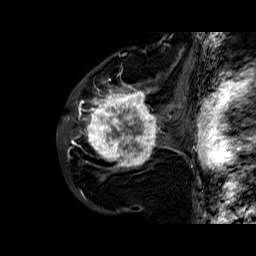
Breast MRI (dynamic contrast-enhanced), one sagittal slice. Position 36 of 60 along the scan axis. Dynamic contrast-enhanced series, time point 2 of 6 at this slice position (early post-contrast). 1.5 T. TE 6.4 ms, TR 32.8 ms. 256 × 256 image matrix. Female patient. From the clinical record (not read from this slice): setting: breast cancer imaged before/during neoadjuvant chemotherapy; receptor status: HR-positive, HER2-negative.
Annotated regions visible in this slice (semi-automatically segmented with operator editing):
- analysis volume of interest (the breast-tissue region the enhancement analysis was run in; not a lesion): bounding box [x1, y1, x2, y2] px = [86, 77, 163, 177]
- tumour enhancement mask (voxels above the 100 % enhancement threshold inside the analysis volume of interest): [86, 78, 159, 169]